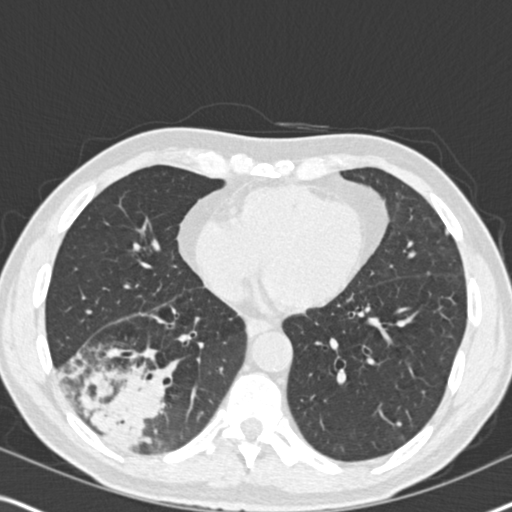
Low-dose screening chest CT, one axial slice. Slice 75 of 182 in the series (ordered by position). Reconstruction kernel B30f. 120 kVp. Lung window (W 1500 / L -600 HU). 2 mm slice thickness. 512 × 512 image matrix, field of view 330 × 330 mm.
Outlined on this slice (expert manual segmentation):
- lesion 1 (tumor, lower lobe of right lung): bounding box [x1, y1, x2, y2] px = [81, 369, 167, 451]